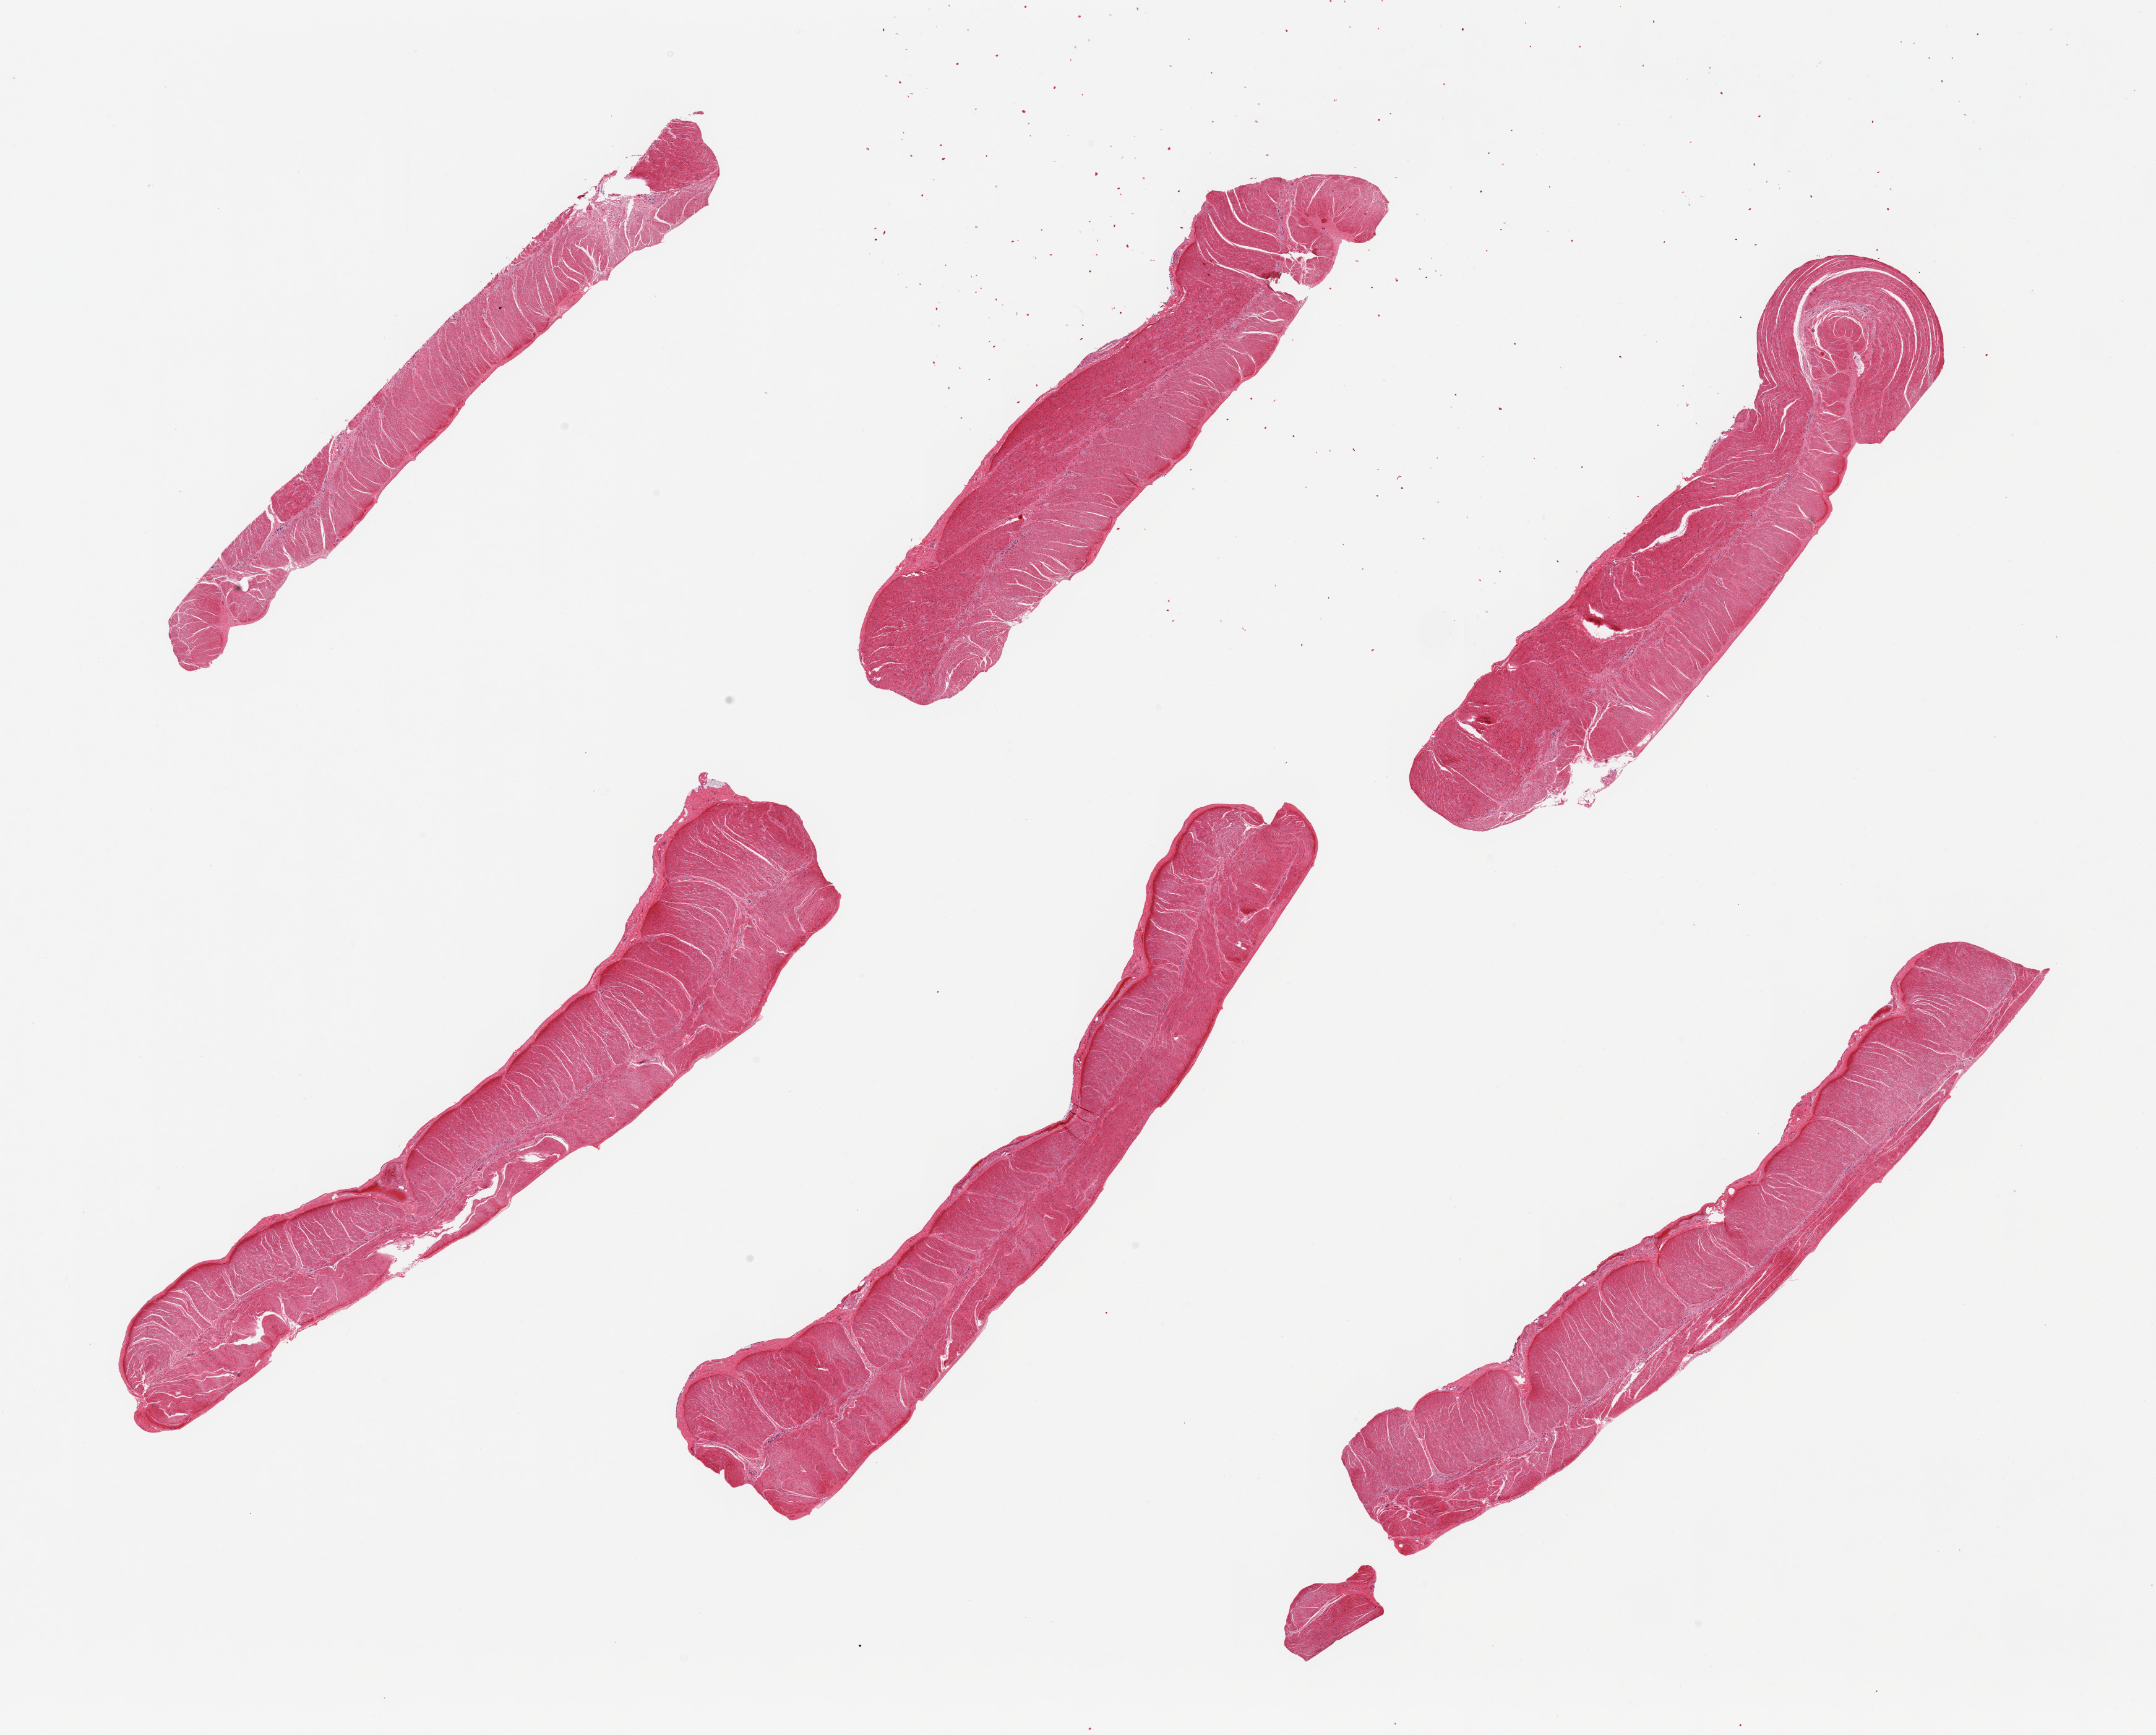
H&E whole-slide image, shown as a low-resolution overview of the whole scanned area (about 27.6 x 22.2 mm, from a 20x scan). PAXgene-fixed, paraffin-embedded tissue. Section of sigmoid colon (target tissue). Donor tissue sample. Donor sex: female.
Reviewer comment on this tissue sample: 6 pieces; well trimmed muscle.